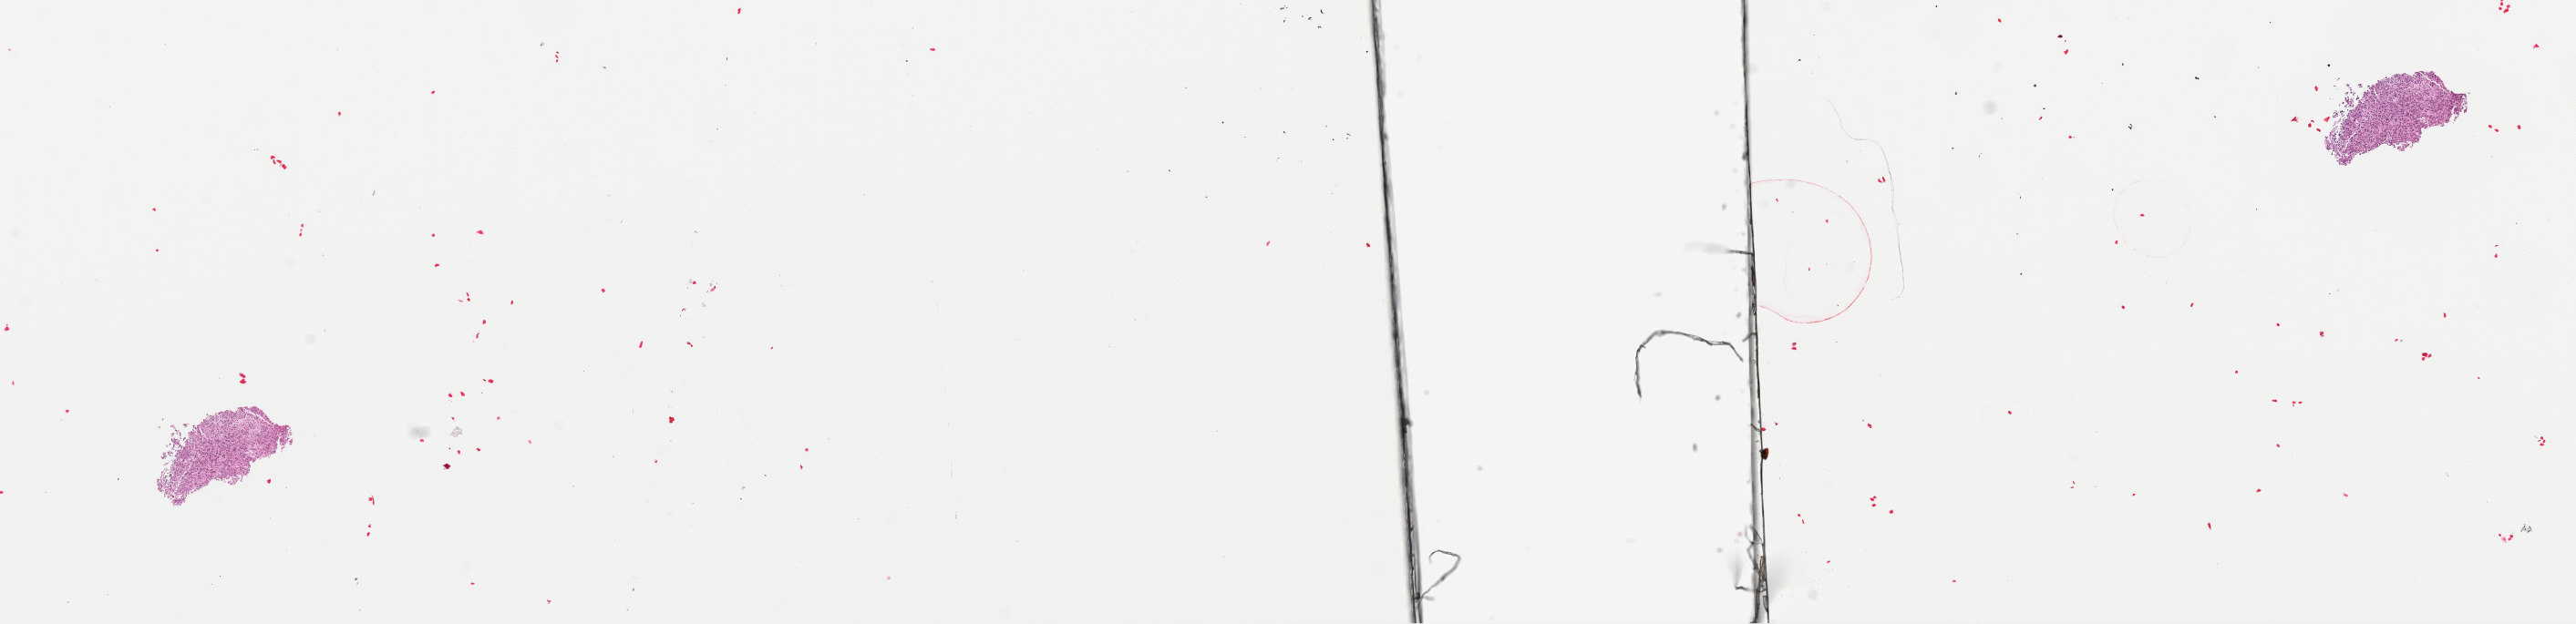
H&E whole-slide image, whole scanned area (about 22.3 x 5.4 mm) shown as a low-resolution overview; frozen section; sample: primary tumour, uterus. Patient: female, age at initial diagnosis 41 years. Pathologist review of this section (percent, as recorded): tumour cells 100%, tumour nuclei 85%, normal cells 0%, stromal cells 0%, necrosis 0%. Inflammatory infiltration, as recorded: lymphocyte infiltration 2%, monocyte infiltration 0%, neutrophil infiltration 0%.
- histologic diagnosis: Leiomyosarcoma, NOS